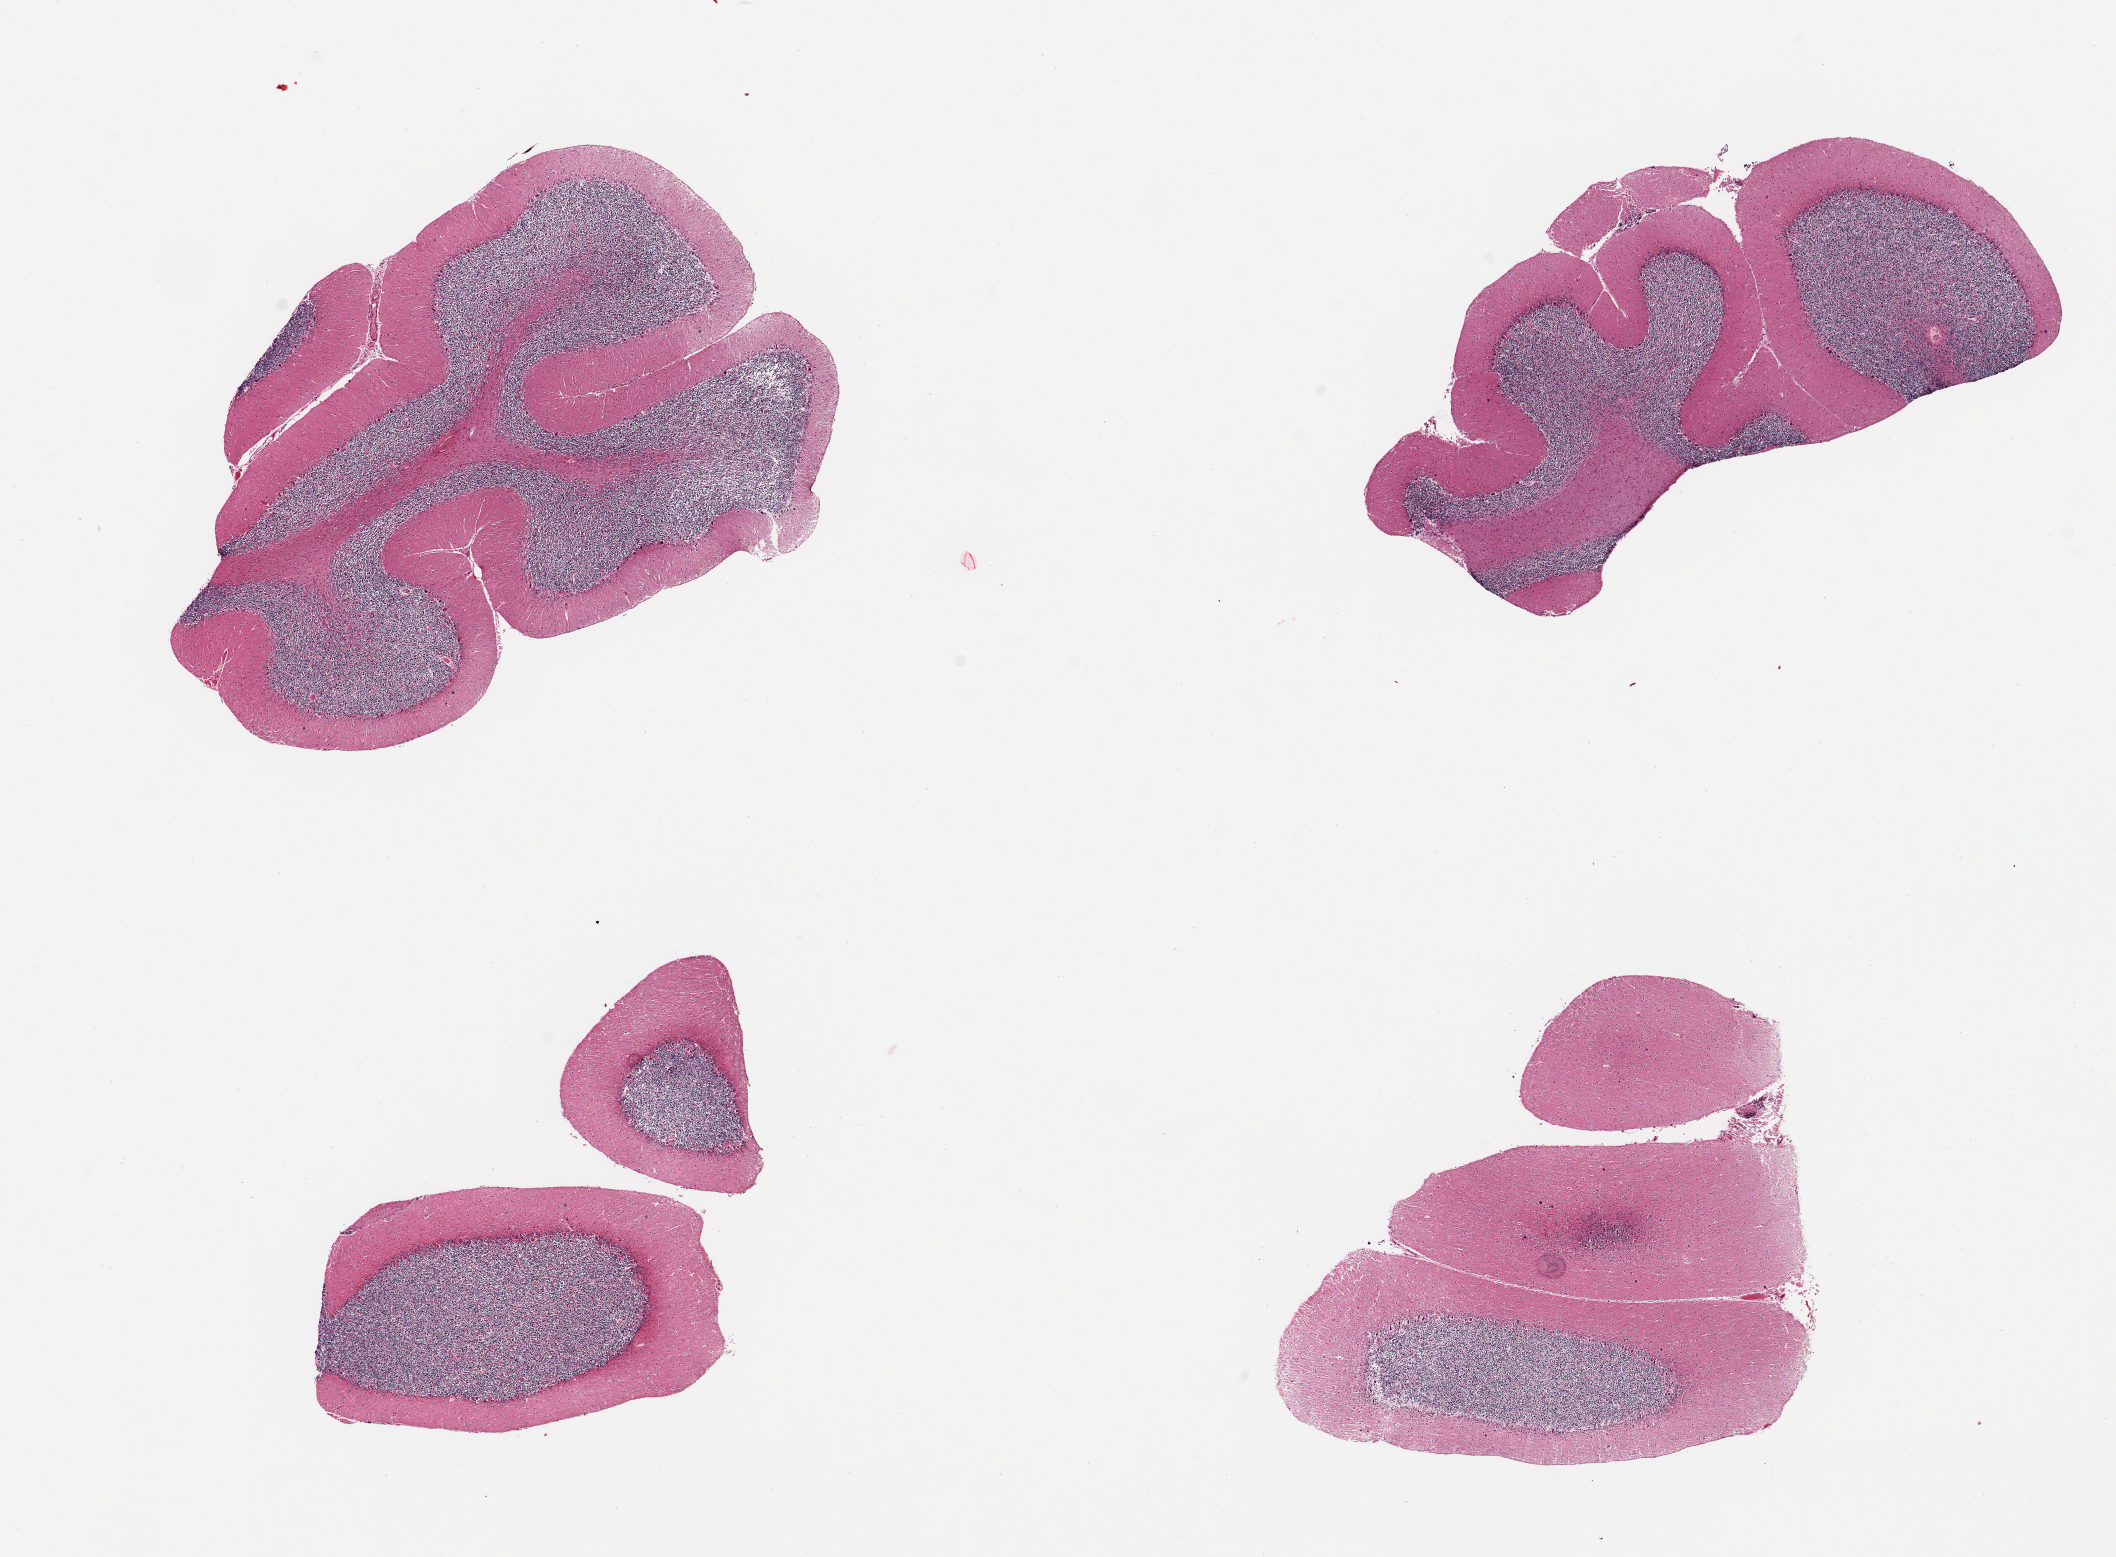
Whole-slide image, hematoxylin and eosin (H&E) stain, brightfield, a low-resolution overview of the entire scanned area, about 16.7 x 12.3 mm, PAXgene-fixed, paraffin-embedded tissue, sampled site (target tissue): cerebellum, tissue donor sample. Female donor.
Reviewer comment on this tissue sample: 4 pieces.